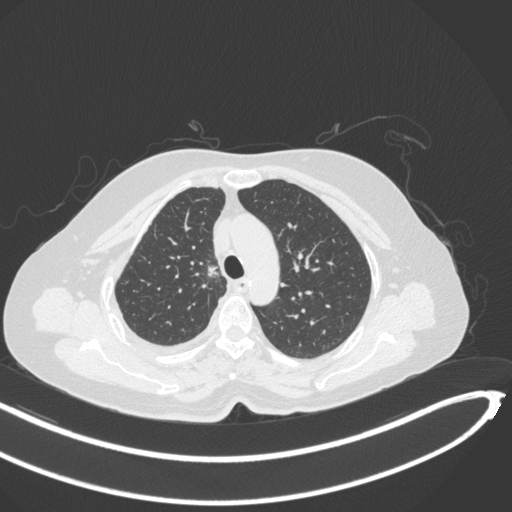
Chest CT, one axial slice; position 229 of 297 along the scan axis; 120 kVp; lung window (W 1500 / L -600 HU); 512 × 512 image matrix, field of view 400 × 400 mm. Female patient, age 64 years. Case-level facts recorded for this patient, not image findings: clinical TNM (as recorded): T1b N0 M1.
Outlined on this slice (bounding box drawn by a radiologist):
- lung tumour (recorded histology: adenocarcinoma): bounding box <201,261,227,282> (left, top, right, bottom; pixels)